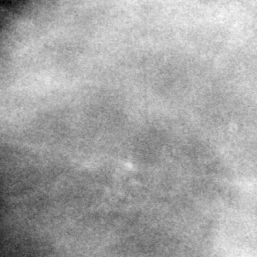
Region of interest cut from a scanned film mammogram (one marked finding), left breast, CC view.
Finding: calcifications, morphology pleomorphic, distribution segmental; BI-RADS assessment category 4; pathology (as recorded): benign.